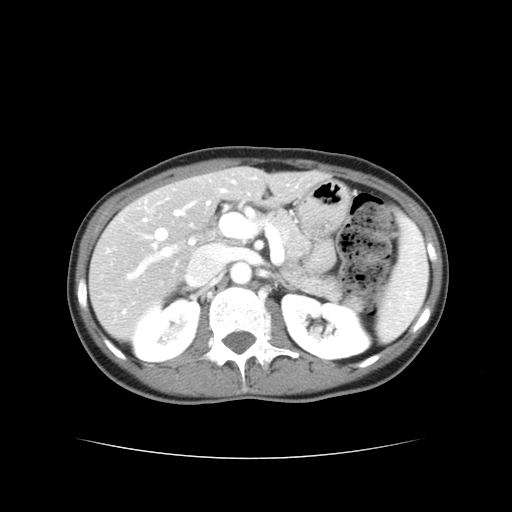
Contrast-enhanced abdominal CT, one axial slice. Position 20 of 38 along the scan axis. Reconstruction kernel STANDARD. 120 kVp. Intravenous contrast given. Soft-tissue window (W 400 / L 40 HU). 512 × 512 image matrix. Female patient, age 54 years. From the clinical record (not read from this slice): diagnosis: colorectal cancer liver metastases, imaged before liver resection; multiple liver metastases: yes; largest metastasis: 1.1 cm.
Annotated regions visible in this slice (manually delineated by an expert):
- hepatic veins: box from (x=128, y=190) to (x=226, y=279) px
- liver: (x=90, y=169)–(x=321, y=336)
- planned liver remnant (the part of the liver to remain after resection): (x=218, y=169)–(x=322, y=202)
- portal vein (with intrahepatic branches): (x=145, y=211)–(x=222, y=257)